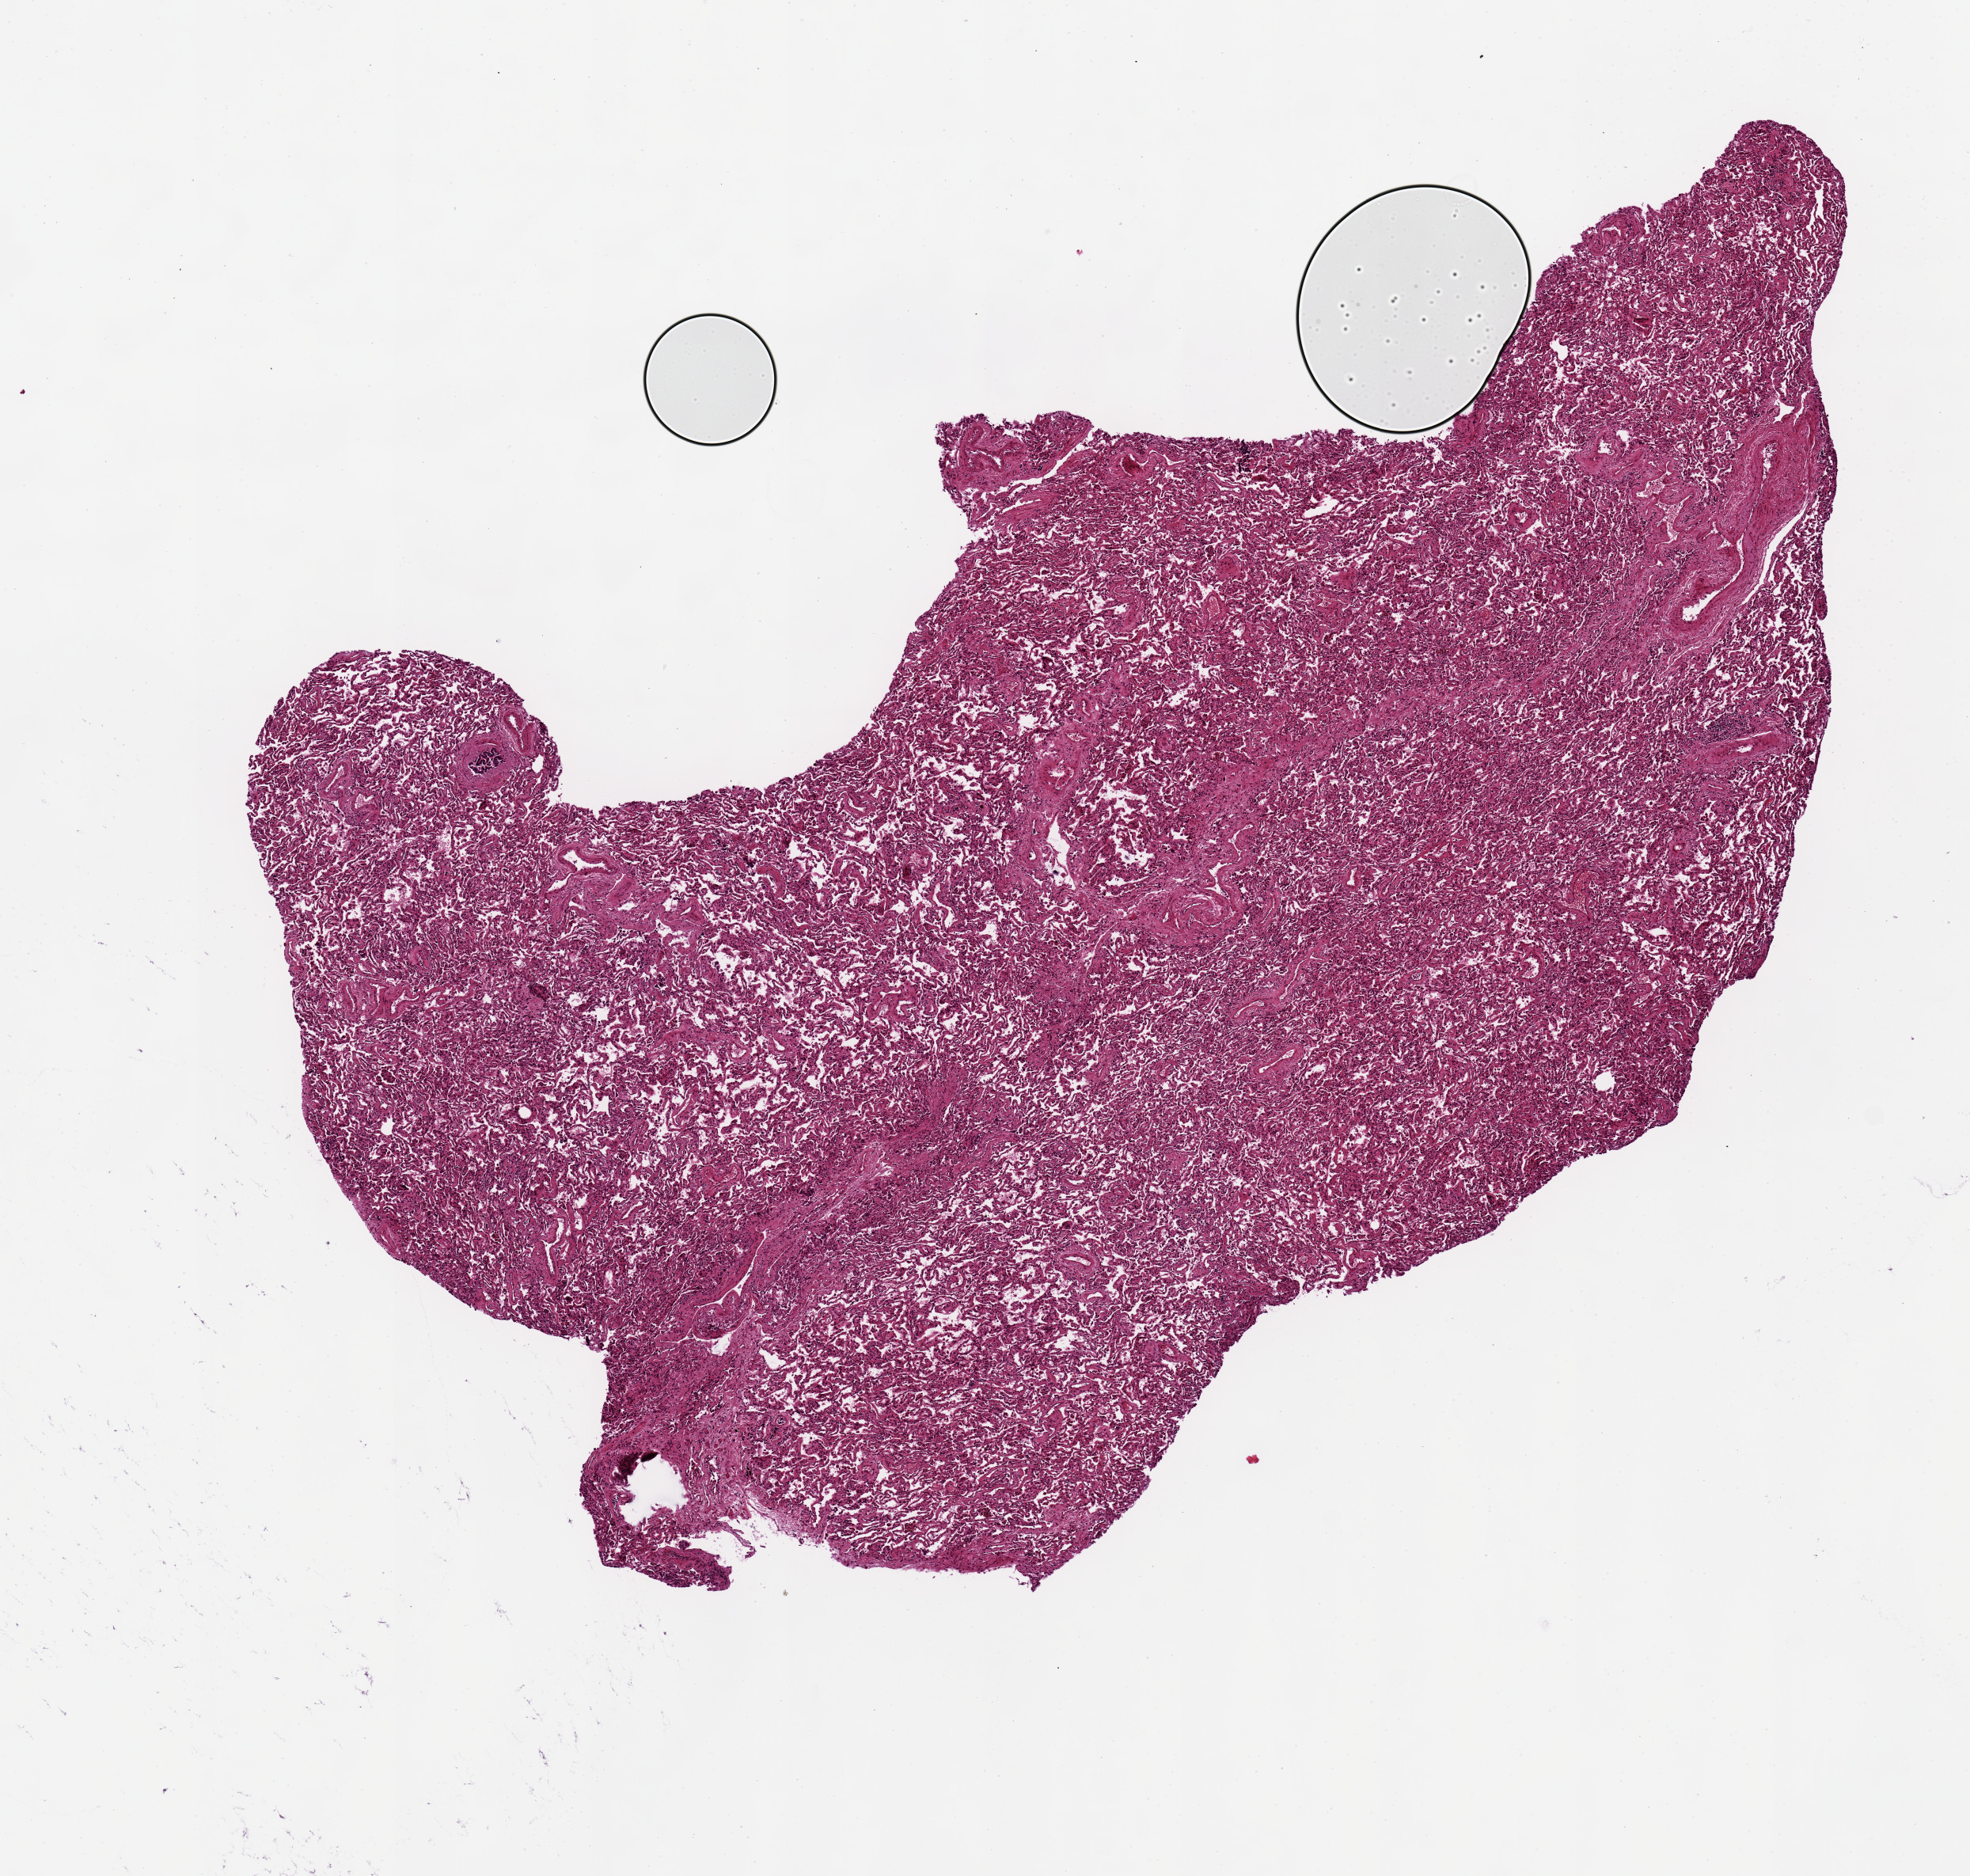
Whole-slide image, hematoxylin and eosin (H&E) stain, shown as a low-resolution overview of the whole scanned area (about 9.8 x 9.4 mm), PAXgene-fixed paraffin-embedded (PFPE) section, section of lung (target tissue), donor tissue sample. Donor sex: male.
• review note (as recorded): Mild alveolar cellular exudates. 8.6x5.8mm aliquot